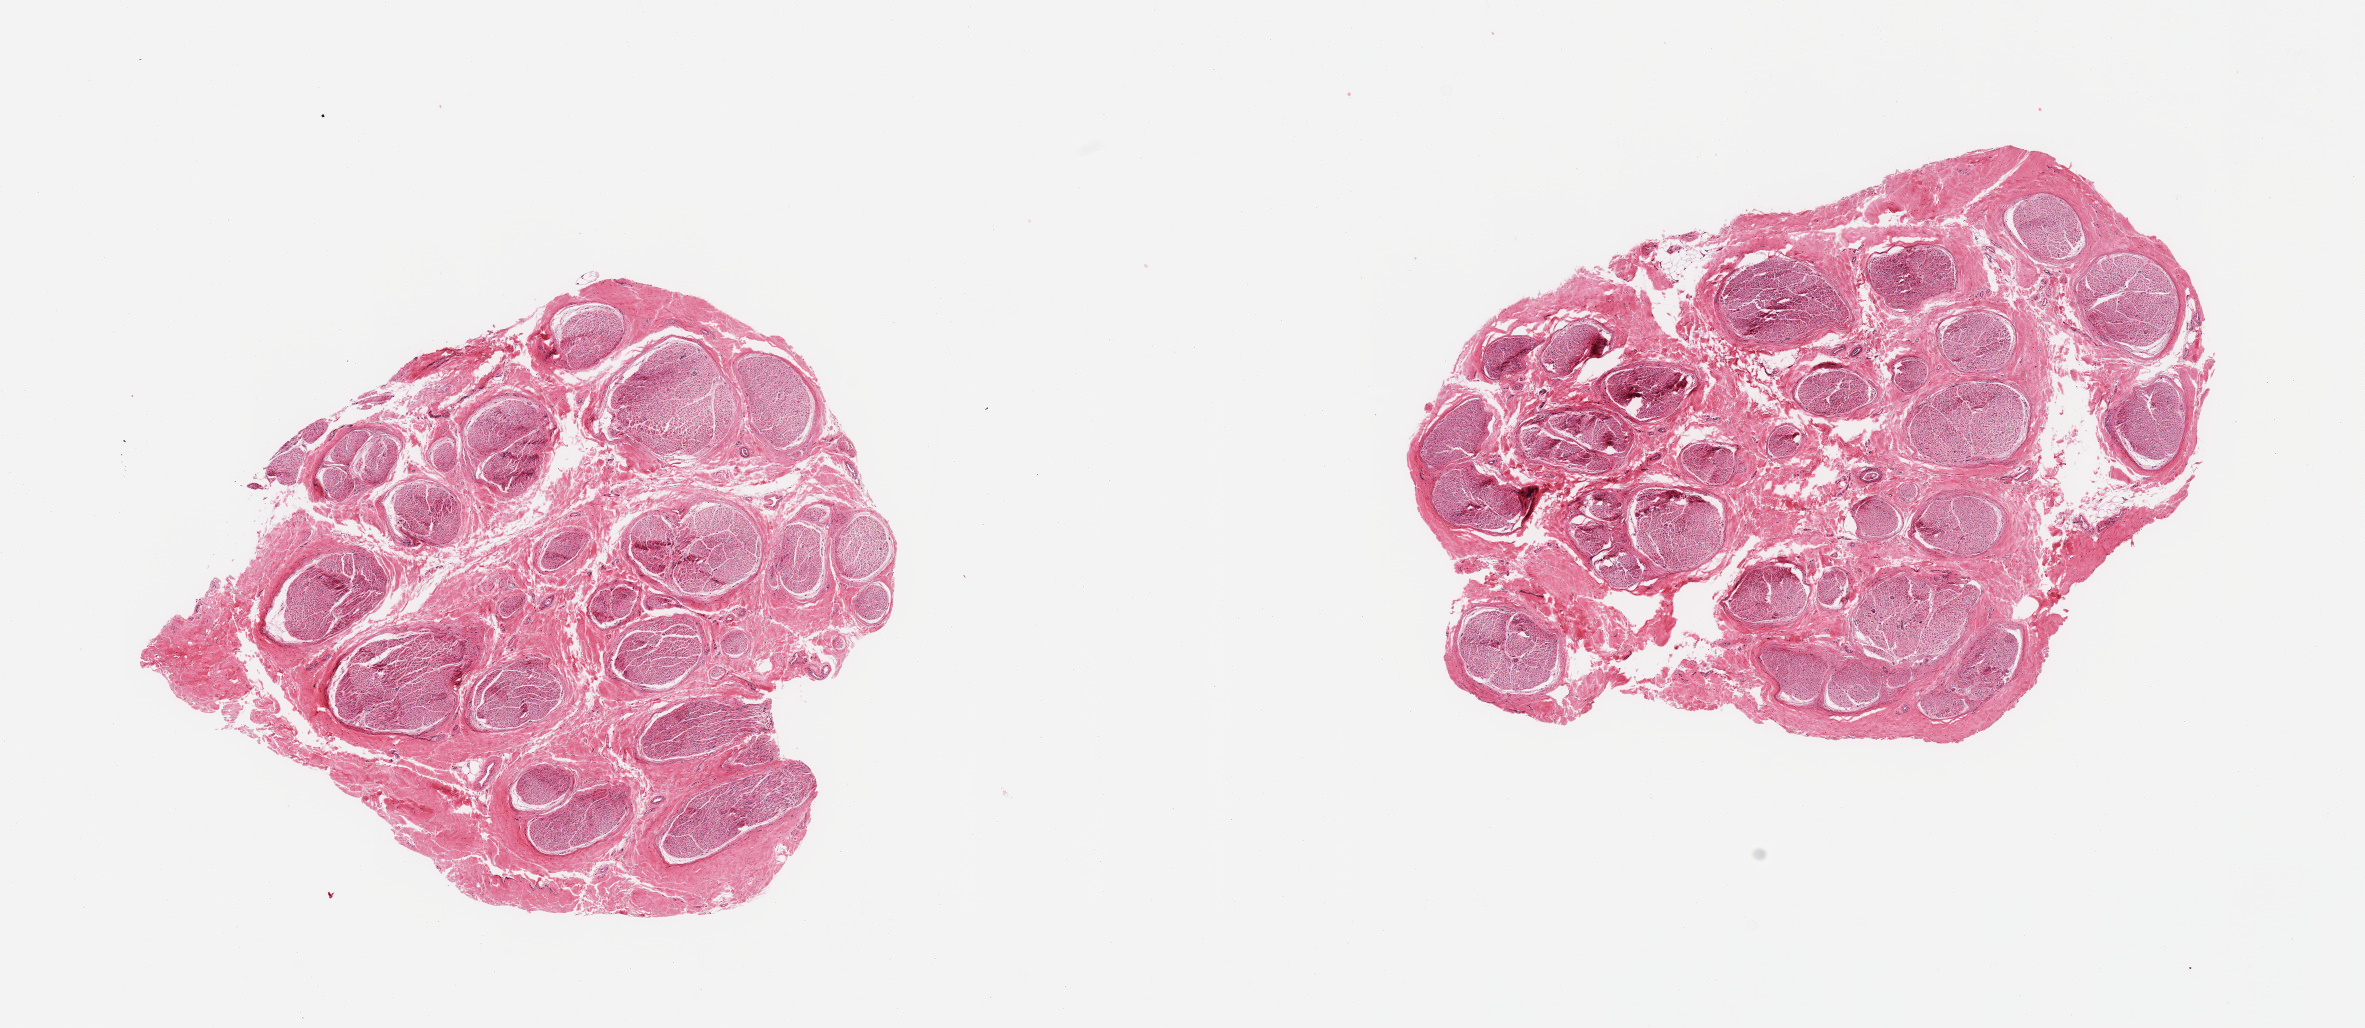
Whole-slide image, haematoxylin and eosin stain — low-resolution overview of the scanned area, about 18.7 x 8.1 mm. PAXgene-fixed, paraffin-embedded tissue. Section of tibial nerve (target tissue). Donor tissue sample. Donor: male.
Pathologist's review note for this sample: 2 pieces, no adherant fat.